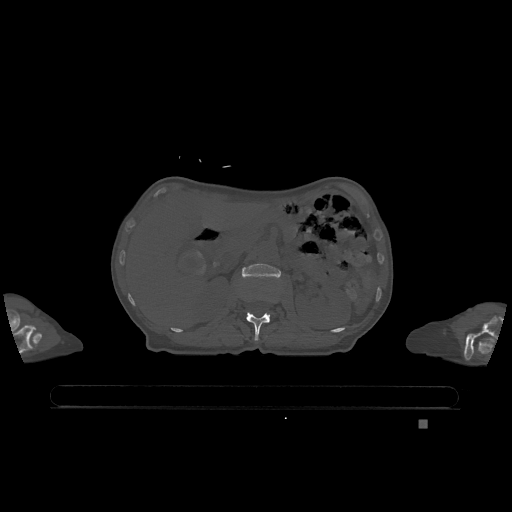
CT including the spine, one axial slice. Position 458 of 1317 along the scan axis. Bone window (W 1800 / L 400 HU). 0.5 mm slice thickness. 512 × 512 image matrix, field of view 500 × 500 mm. Female patient, age 74 years. From the clinical record (not read from this slice): primary cancer: lung.
Structures marked on this image (semi-automatic segmentation, software-assisted and operator-edited):
- L1 vertebra: bounding box [x1, y1, x2, y2] px = [246, 312, 270, 341]
- L2 vertebra: [242, 264, 281, 278]